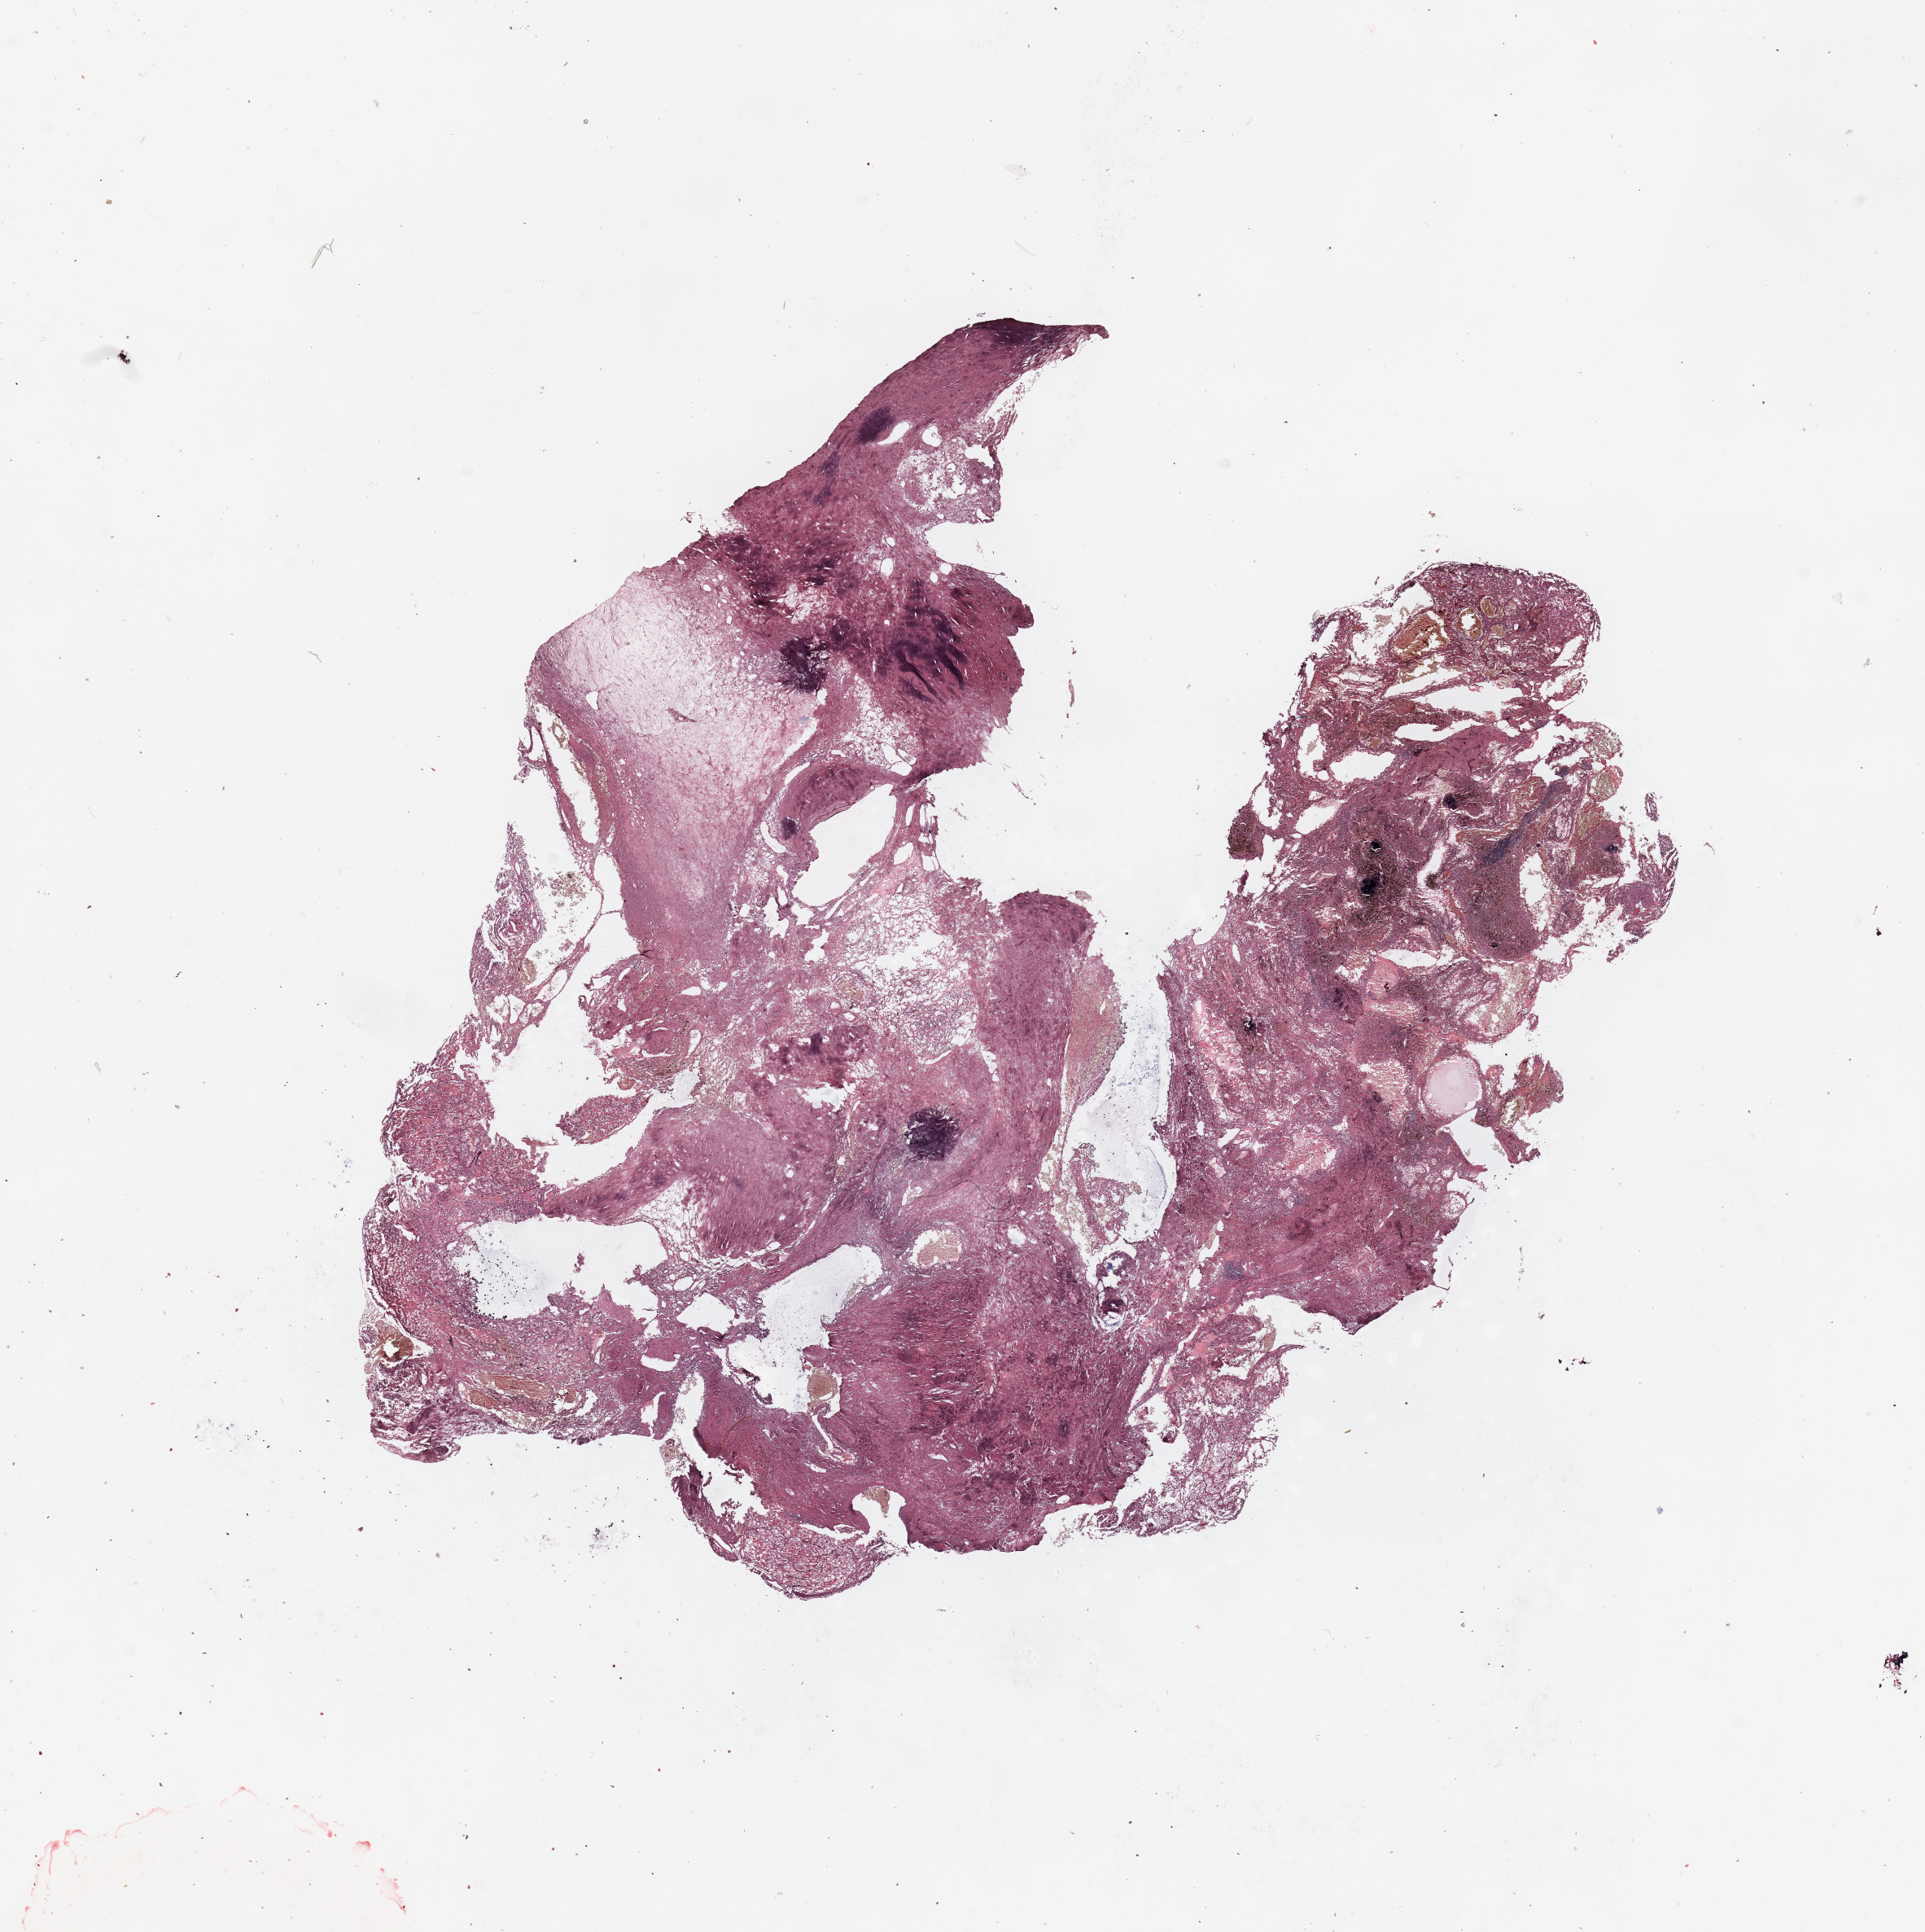
H&E-stained whole-slide image, low-resolution overview of the scanned area, about 18.7 x 18.8 mm (from a 20x scan), tumour tissue sample, sampled site: kidney. 60-year-old male patient. Histologic grade: G2 (moderately differentiated). Composition of this section per pathologist review: tumour nuclei 50%, necrosis 60%.
Histologic diagnosis: Renal cell carcinoma, NOS. AJCC pathologic stage: II. Primary tumour site (as recorded): upper pole.